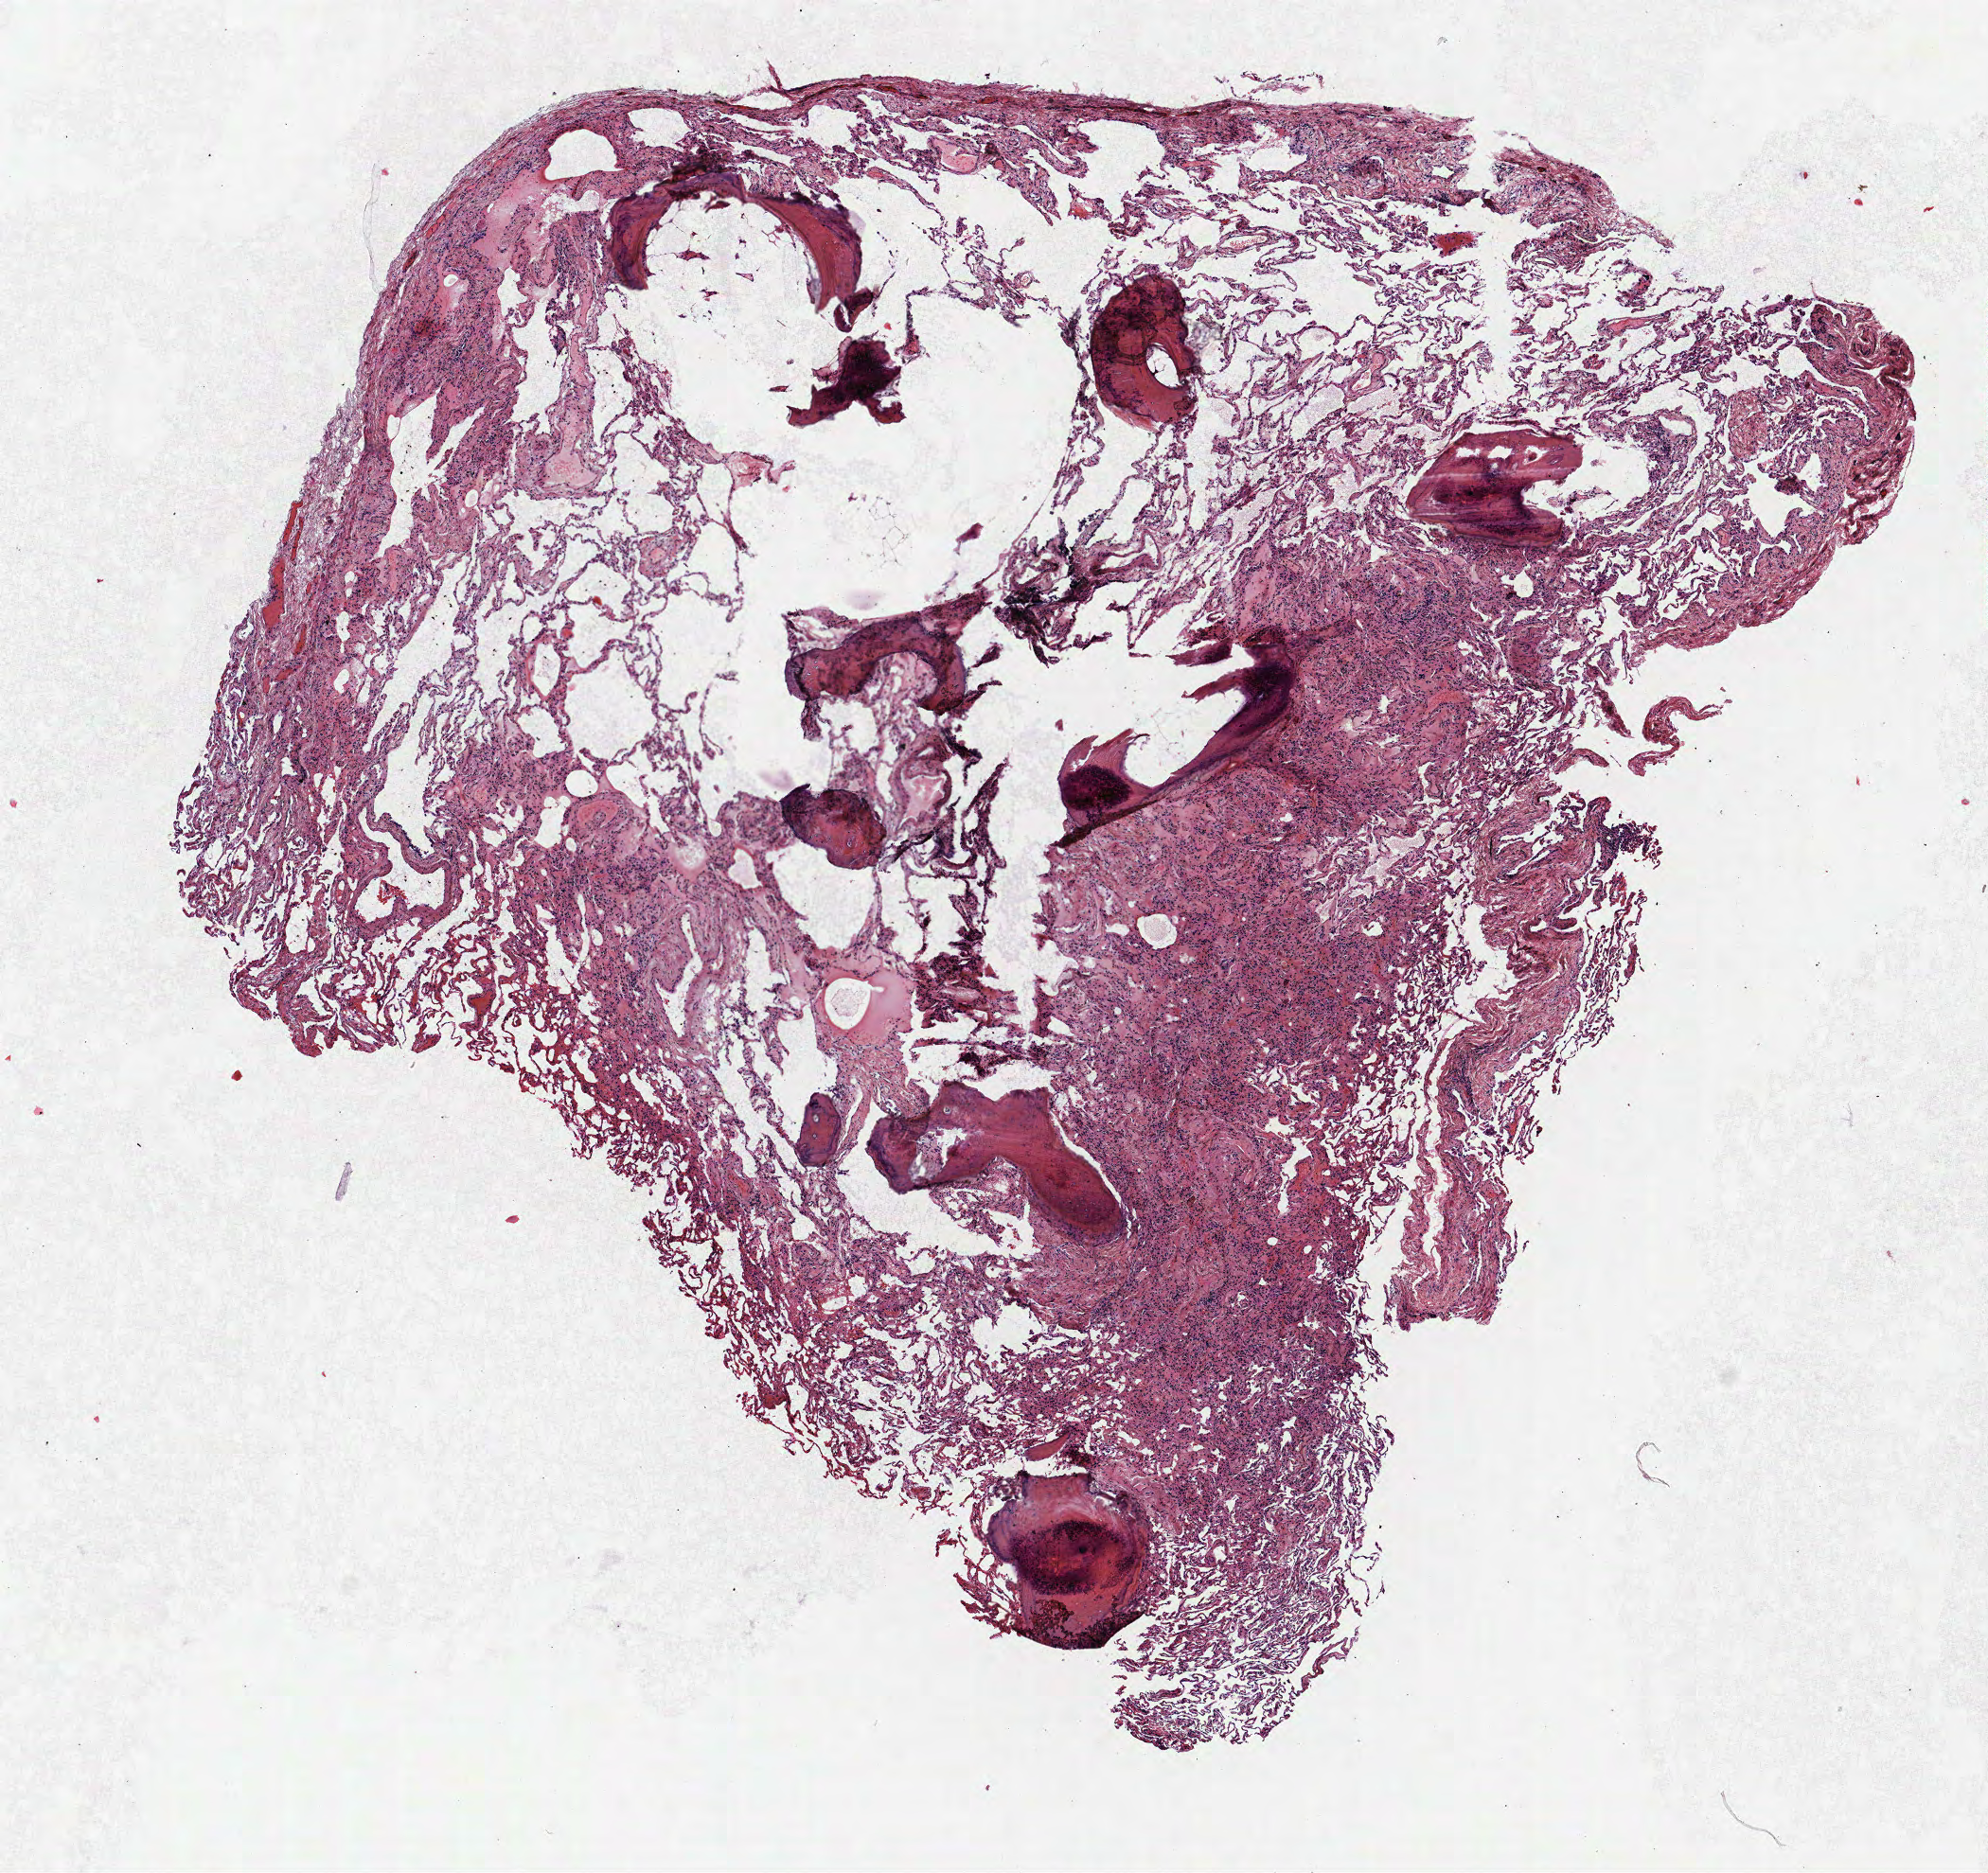
H&E-stained whole-slide image, shown as a low-resolution overview of the whole scanned area (about 8.4 x 7.9 mm), formalin-fixed paraffin-embedded (FFPE) section, lung tissue. Male, age 68 at enrolment. Grade: poorly differentiated (G3).
• stage (AJCC 6th edition): IIIA
• tumour size (pathology): 30 mm
• participant's lung-cancer diagnosis: Adenosquamous carcinoma
• ICD-O-3 topography: lower lobe of lung (C34.3)
• primary tumour location (clinical record): right lower lobe